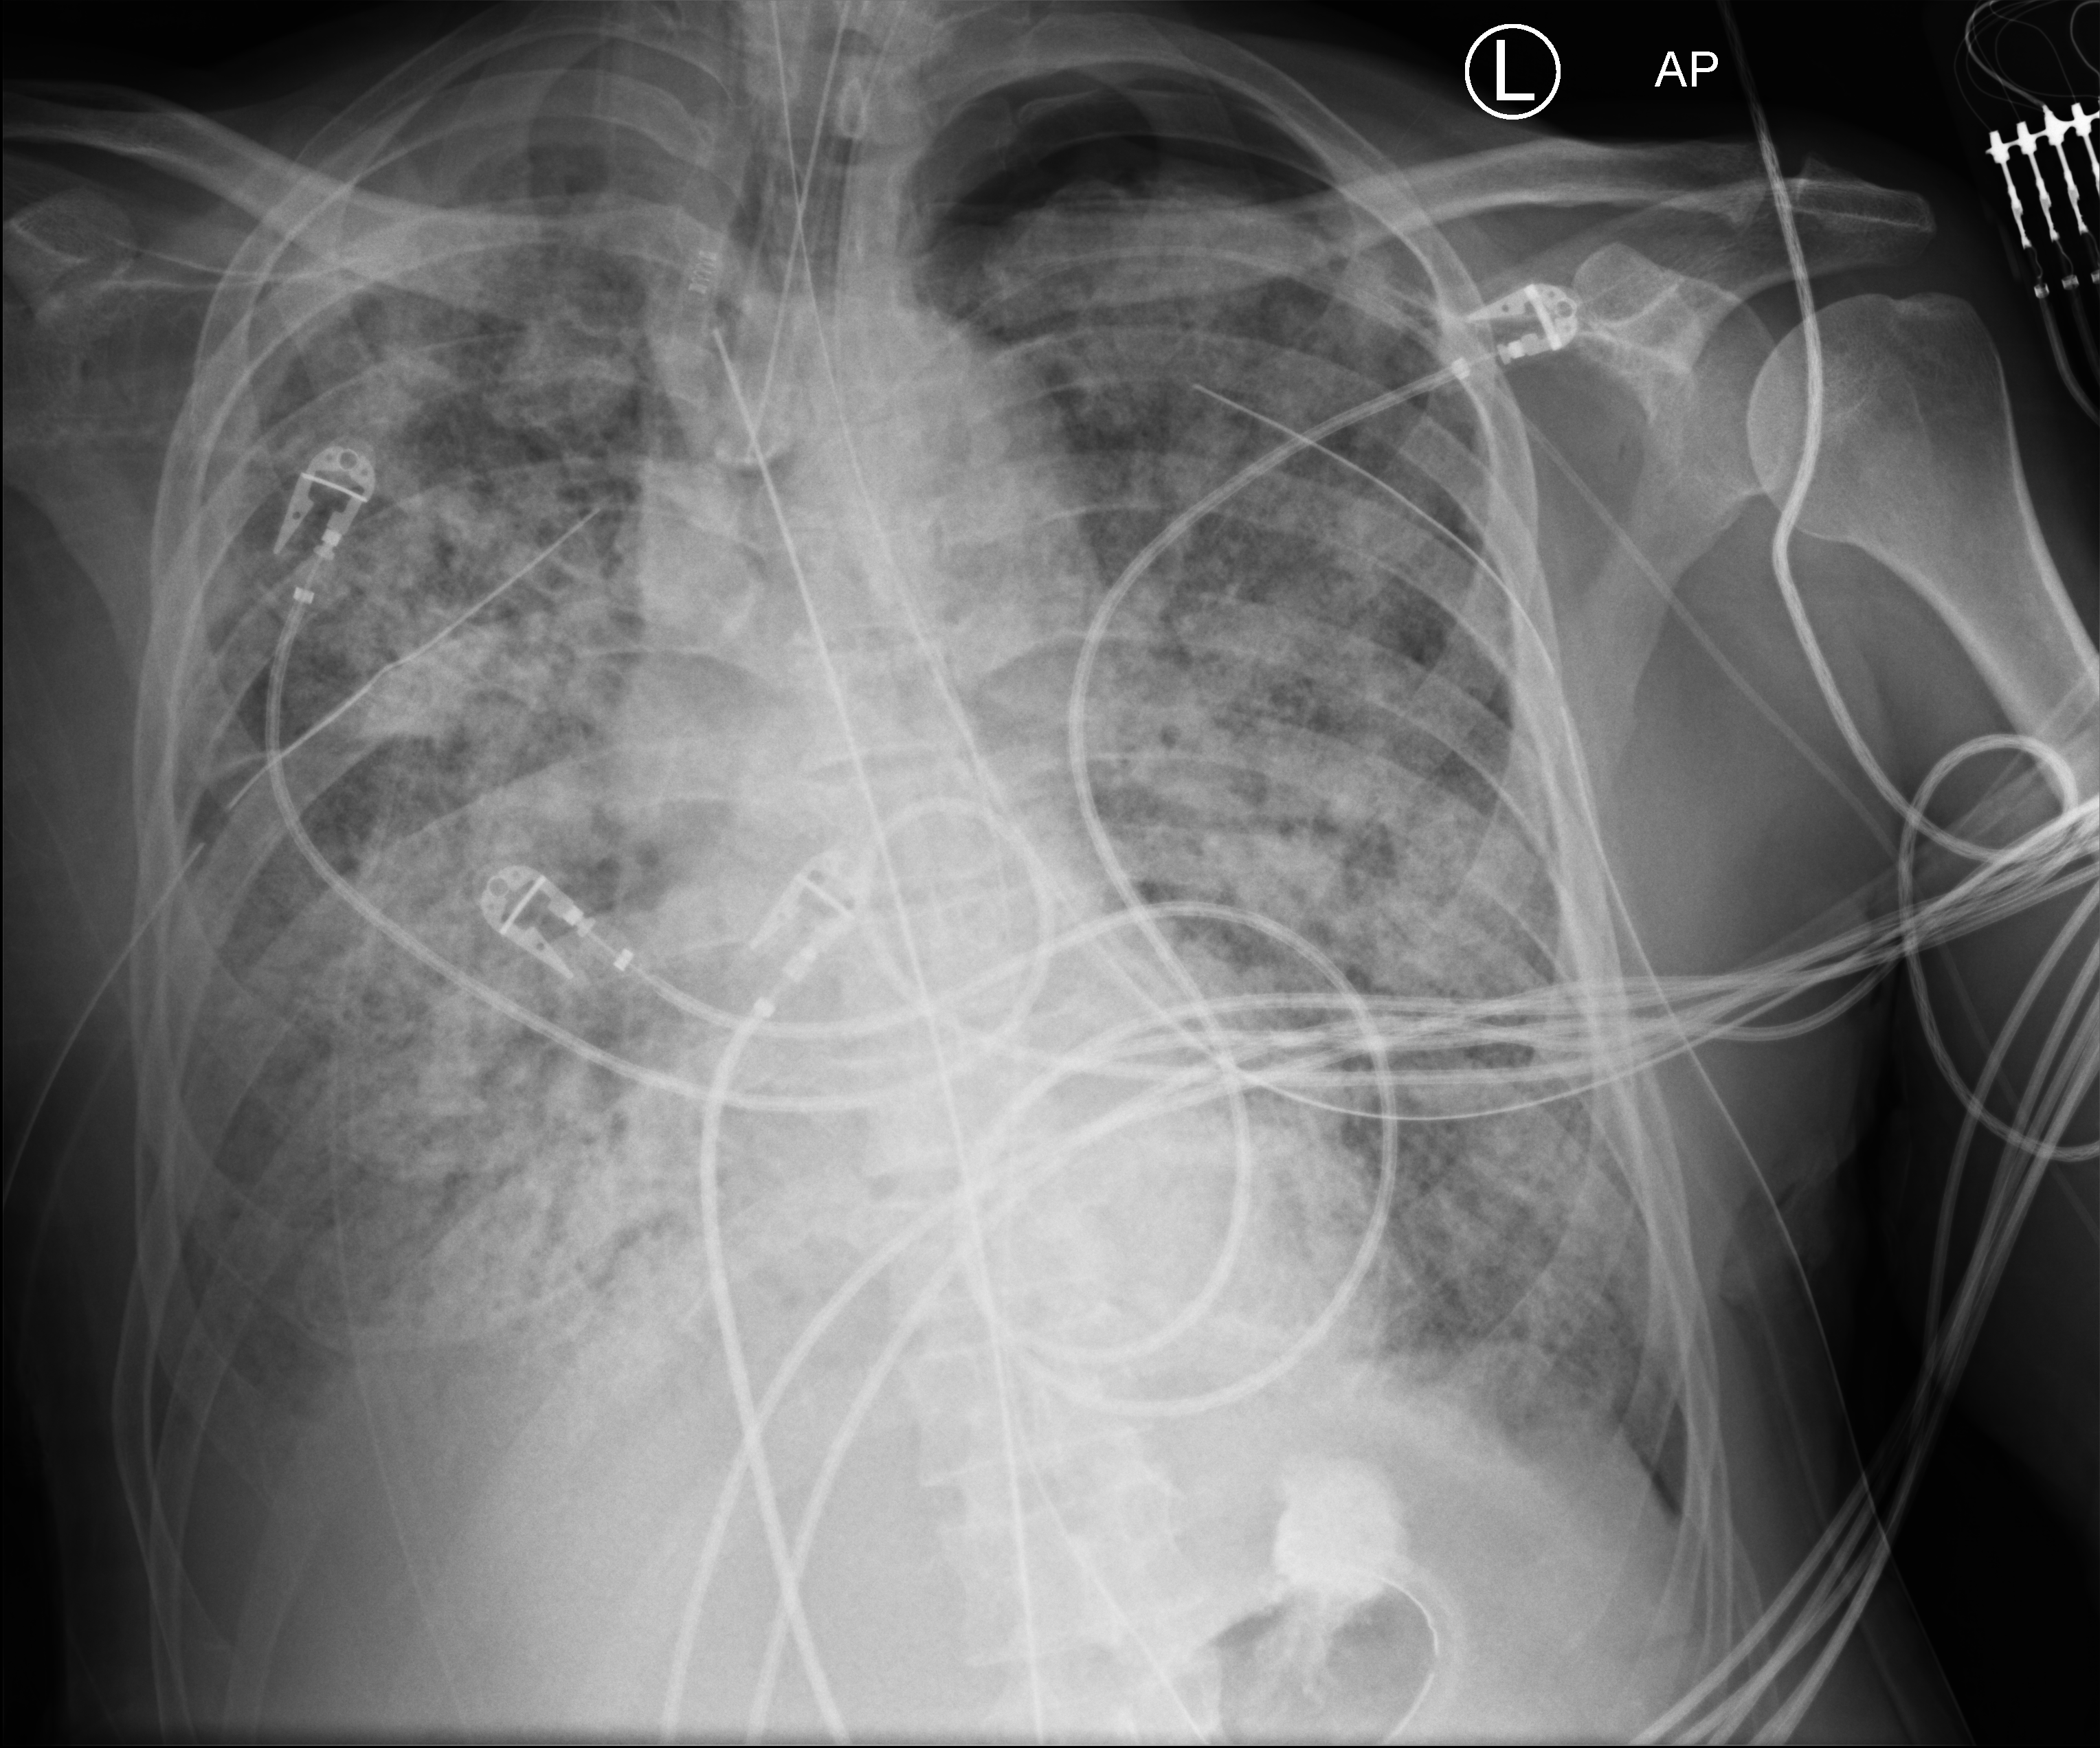
Chest X-ray (portable). Male patient hospitalised with COVID-19, age 60–74 years.
From the hospital-stay record, not from the radiograph (when in the stay this image was taken is not recorded):
- admitted to intensive care during this hospital stay: yes